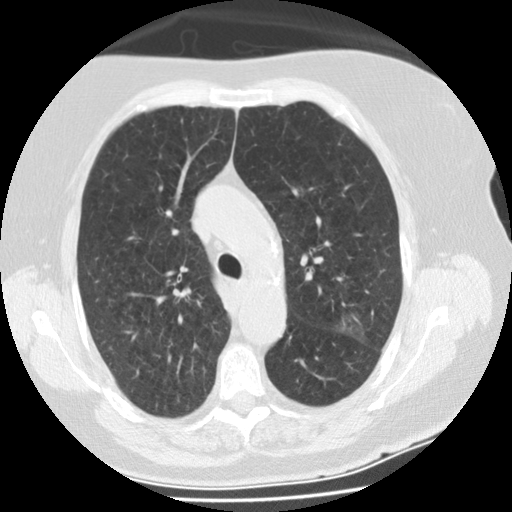
Chest CT (low-dose screening protocol), one axial image. Second annual screen. Lung window (W 1500 / L -600 HU). 2.5 mm slice thickness. Standard (soft-tissue) reconstruction kernel (STANDARD). 120 kVp. Slice 84 of 297 in the series. 512 × 512 image matrix, field of view 321 × 321 mm. Female, age 74 years at enrolment. Former smoker at enrolment.
Expert reader's lesion annotation, bounding box [x1, y1, x2, y2] px = [326, 303, 388, 359]. The screening reader recorded 3 non-calcified nodules or masses ≥4 mm on this exam (right lower lobe, left upper lobe, left upper lobe); which of them this box marks is not recorded. Participant outcome: lung cancer diagnosed 68 days after this screen — bronchiolo-alveolar adenocarcinoma, NOS, left upper lobe, stage IA (AJCC 6th edition), 20 mm at pathology.